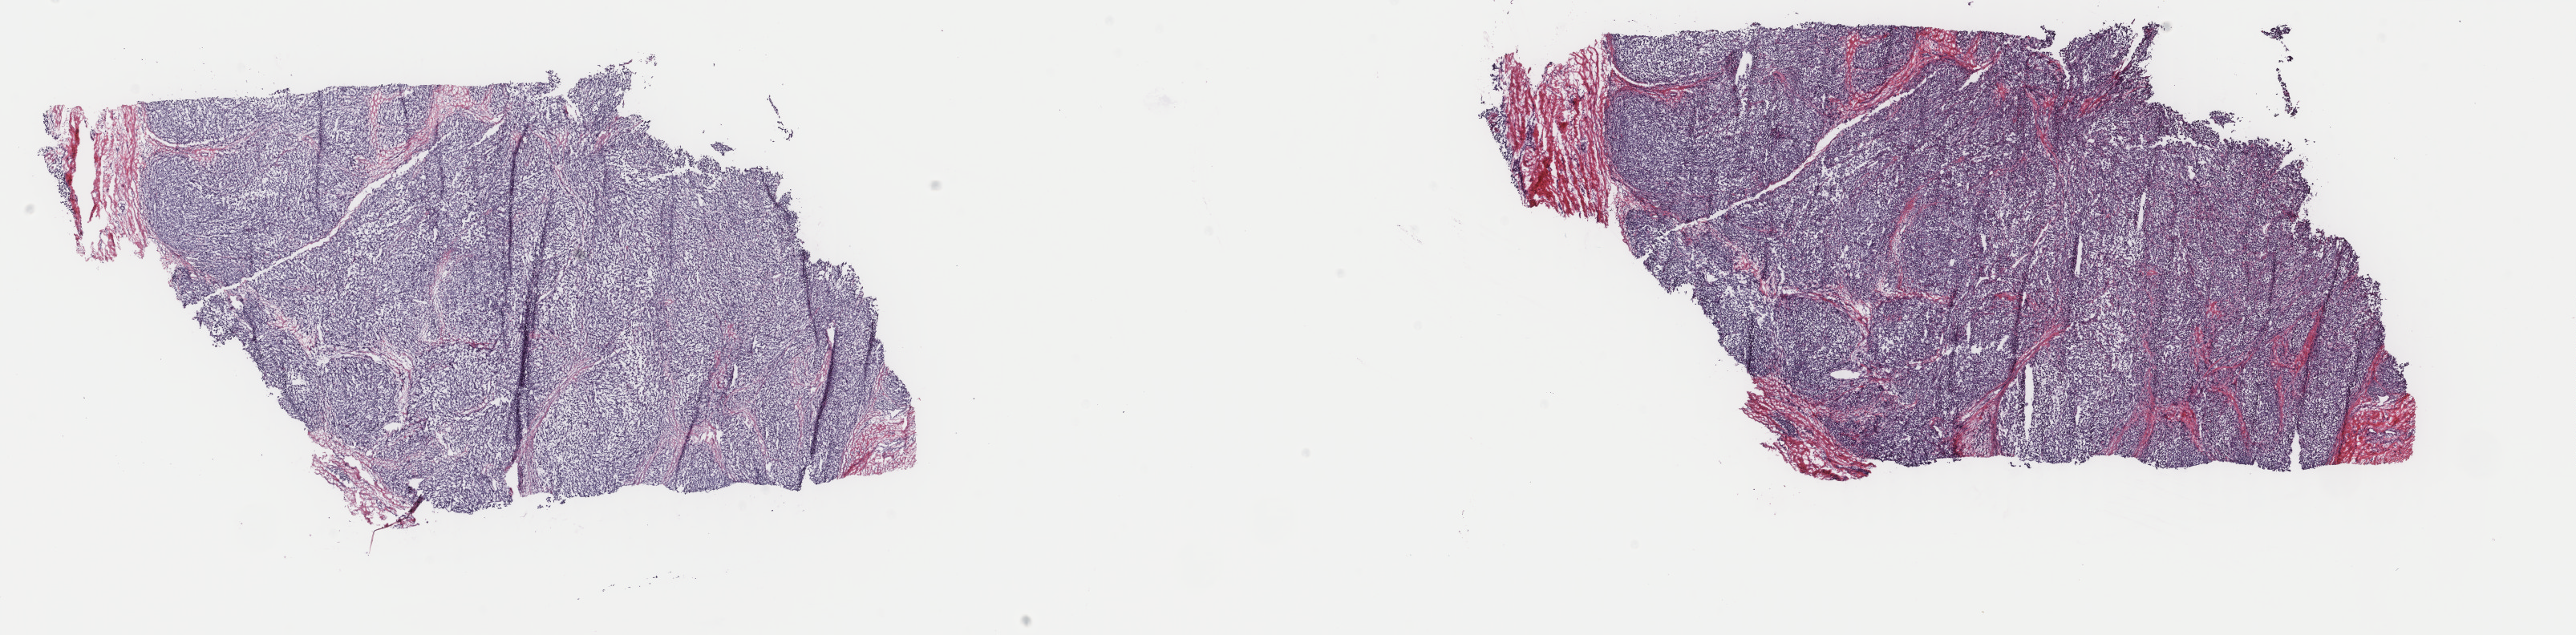
H&E-stained whole-slide image, a low-resolution overview of the entire scanned area, about 25.5 x 6.3 mm (slide scanned at 40x); frozen section from the top of the tissue portion; metastatic tumour sample, sampled site: lymph nodes of inguinal region or leg. Male patient; age at initial diagnosis 52 years. Composition of this section per pathologist review: tumour cells 100%, tumour nuclei 85%, normal cells 0%, stromal cells 0%, necrosis 0%. Infiltration values recorded for this section: lymphocyte infiltration 1%, monocyte infiltration 0%, neutrophil infiltration 0%.
This section: metastatic tumour tissue. Patient diagnosis: Malignant melanoma, NOS.